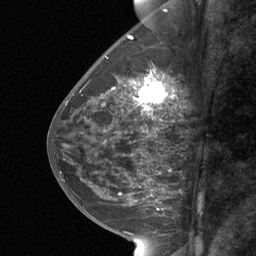
Breast MRI (dynamic contrast-enhanced), one sagittal slice; dynamic contrast-enhanced study with each time point stored as its own series, time point 2 of 3 at this slice position (early post-contrast, ordered by acquisition time); 1.5 T; TE 4.8 ms, TR 27 ms; 2 mm slice thickness; 256 × 256 image matrix, field of view 180 × 180 mm. Patient: female, 59 years. Case-level facts recorded for this patient, not image findings: setting: breast cancer imaged before/during neoadjuvant chemotherapy; receptor status: triple-negative.
Structures marked on this image (semi-automatic segmentation, software-assisted and operator-edited):
- analysis volume of interest (the breast-tissue region the enhancement analysis was run in; not a lesion): box from (x=129, y=66) to (x=171, y=122) px
- tumour enhancement mask (voxels above the 90 % enhancement threshold inside the analysis volume of interest): (x=134, y=78)–(x=168, y=111)